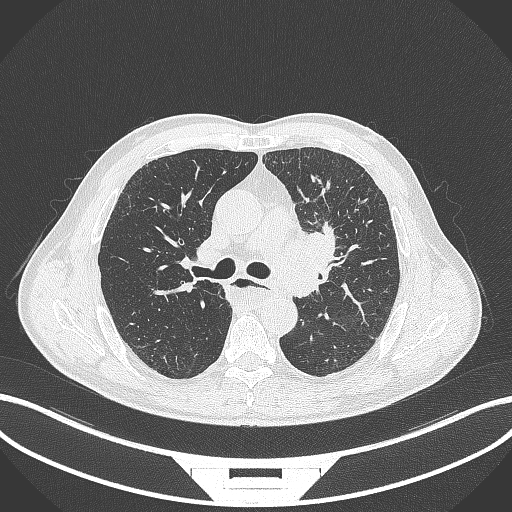
Chest CT, one axial slice. Slice 239 of 411 in the series (ordered by position). Reconstruction kernel B70f. Lung window (W 1500 / L -600 HU). 1 mm slice thickness. 512 × 512 image matrix, field of view 400 × 400 mm. Male patient, age 57 years. From the clinical record (not read from this slice): clinical TNM (as recorded): T2a N1 M0.
Structures marked on this image (rectangle marked by the reading radiologist):
- lung tumour (recorded histology: squamous cell carcinoma): bounding box (x1, y1, x2, y2) in pixels: (268, 222, 345, 302)